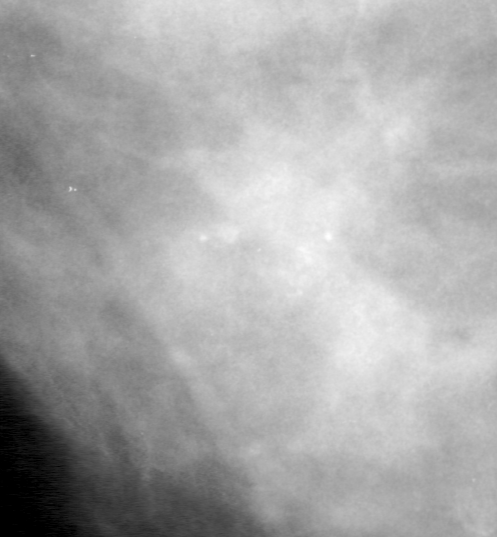
Cropped region of a digitized screen-film mammogram centred on a radiologist-marked abnormality; left breast; MLO view; BI-RADS breast density category 4 (scale 1–4).
Marked abnormality: calcifications, morphology amorphous, distribution clustered; BI-RADS assessment category 4; pathology result (as recorded, not read from the image): benign.